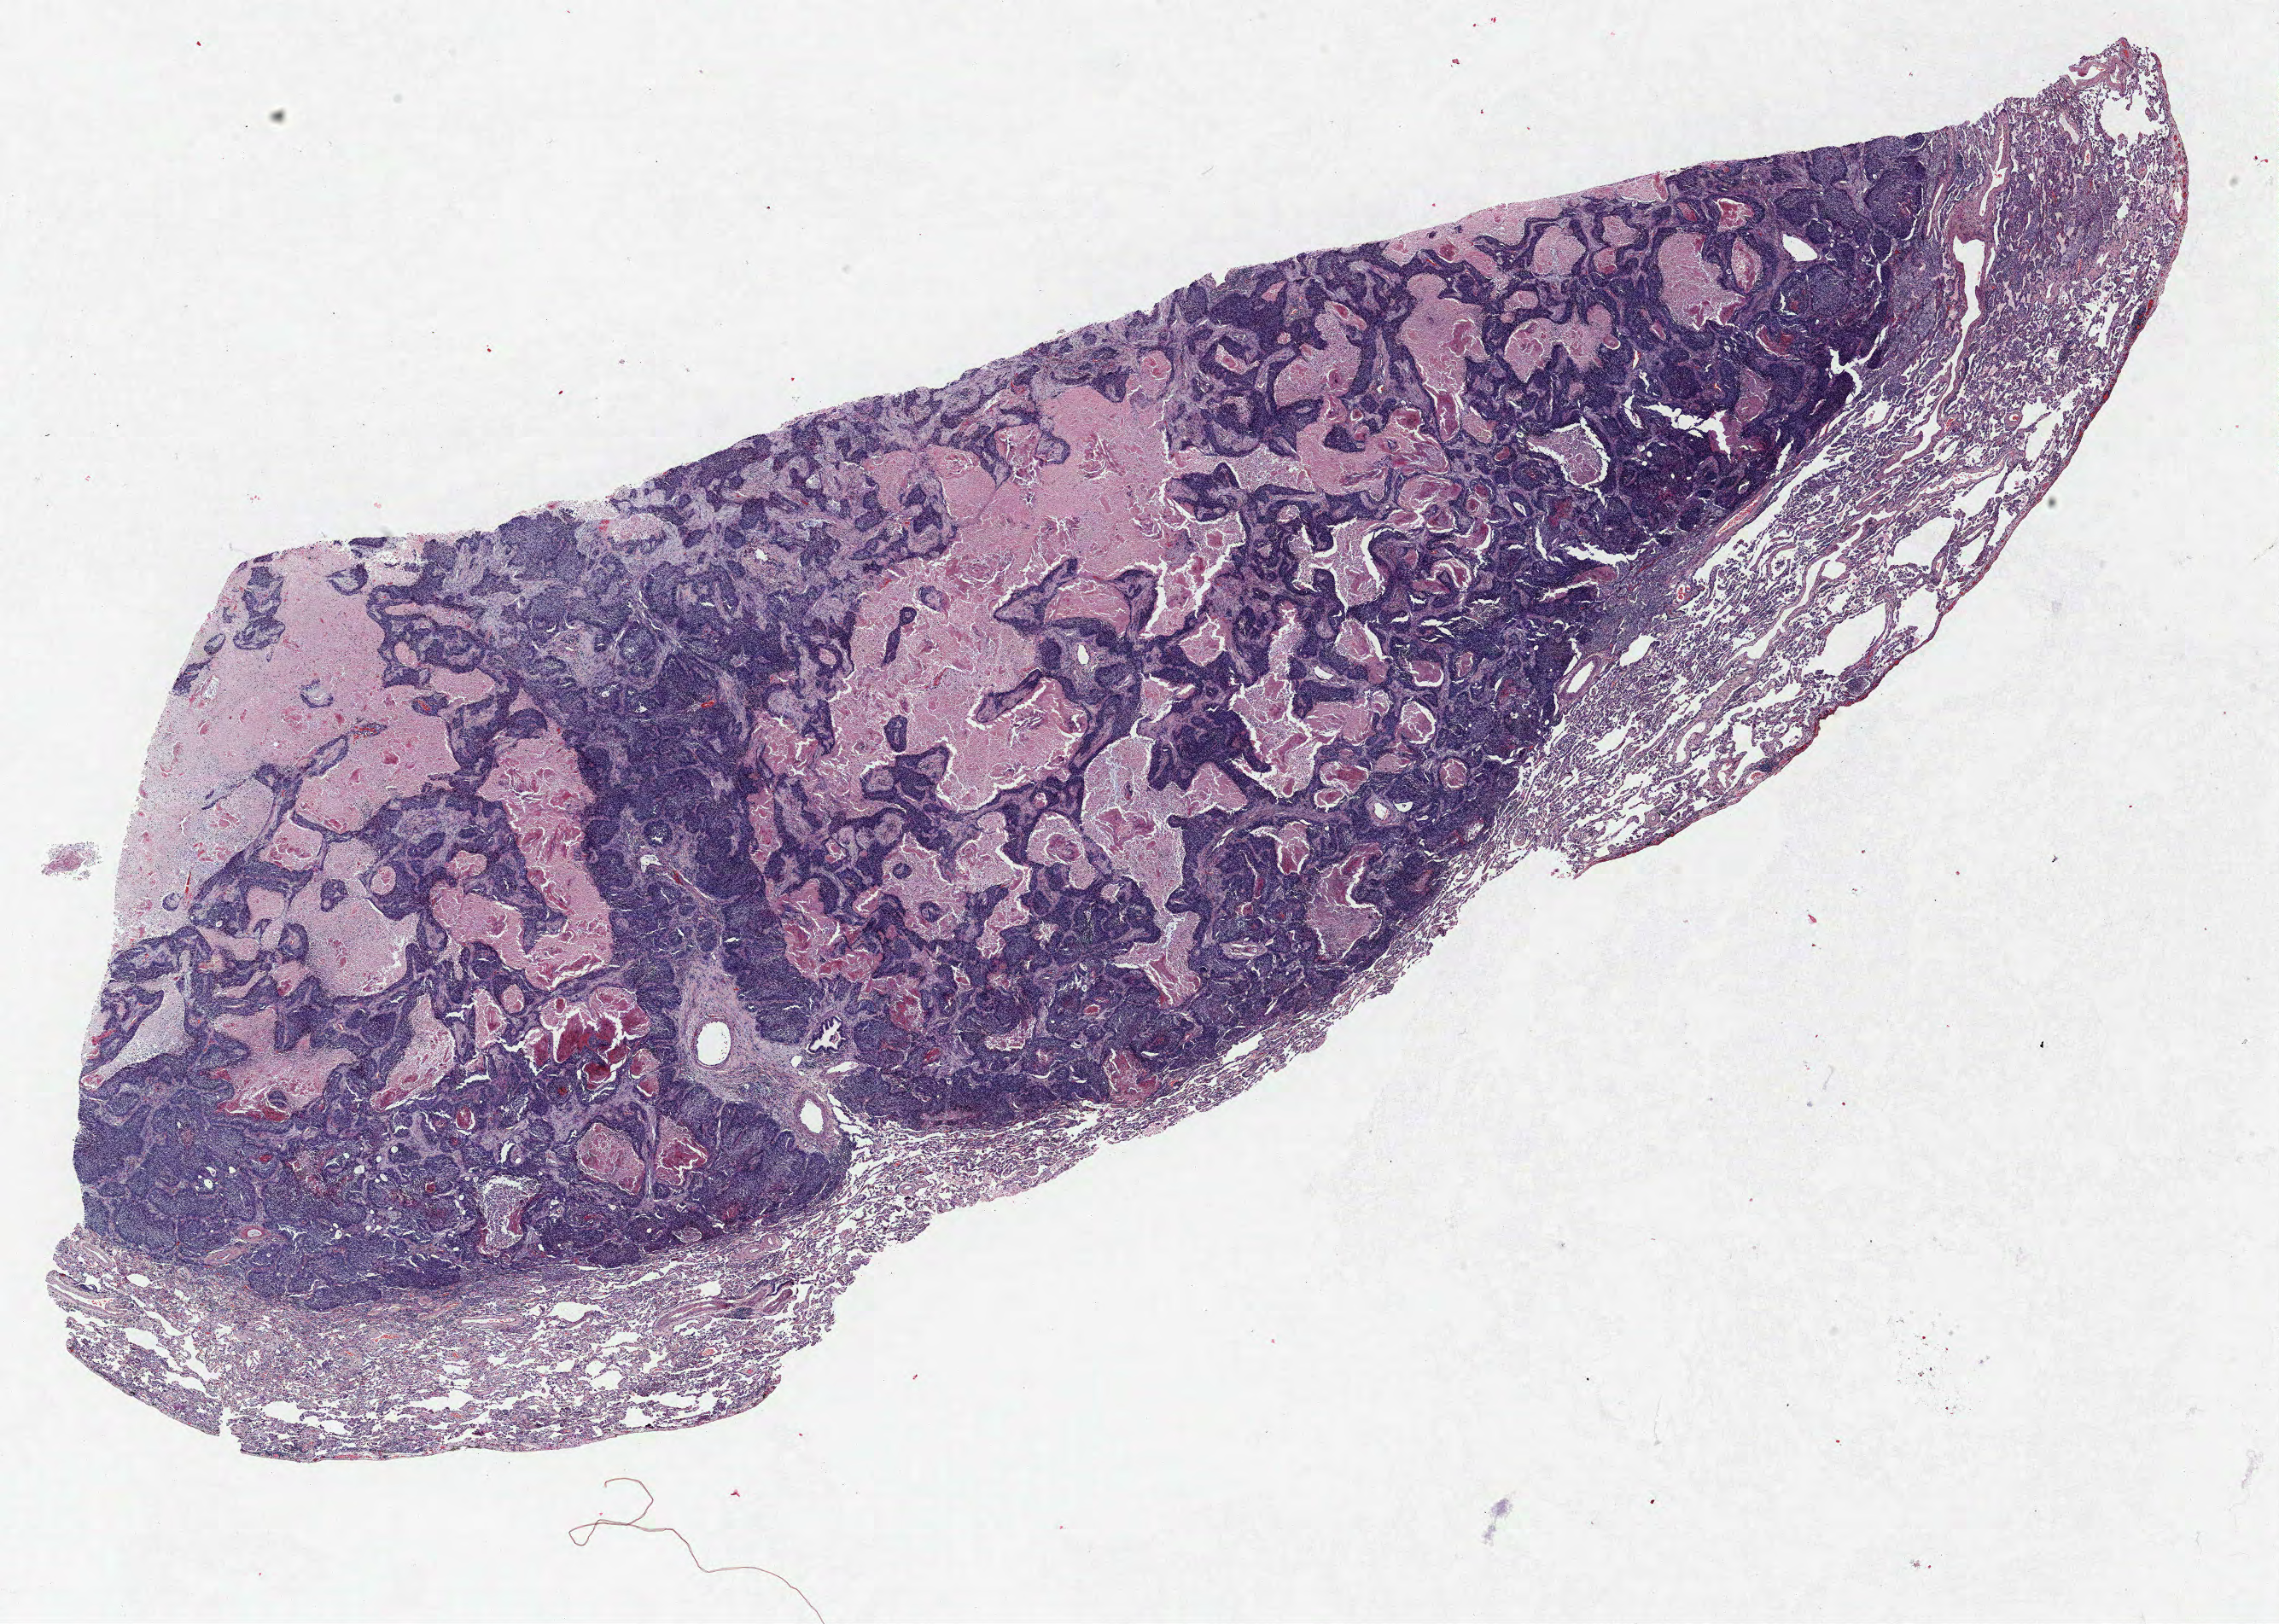
H&E whole-slide image, whole scanned area (about 21.4 x 15.2 mm) shown as a low-resolution overview, formalin-fixed paraffin-embedded (FFPE) section, lung tissue. Male, age 62 at enrolment. Former smoker at enrolment. Grade: poorly differentiated (G3).
Tumour size (pathology): 45 mm. Primary tumour location (clinical record): right lower lobe. Stage (AJCC 6th edition): IB. Participant's lung-cancer diagnosis: Squamous cell carcinoma, NOS.